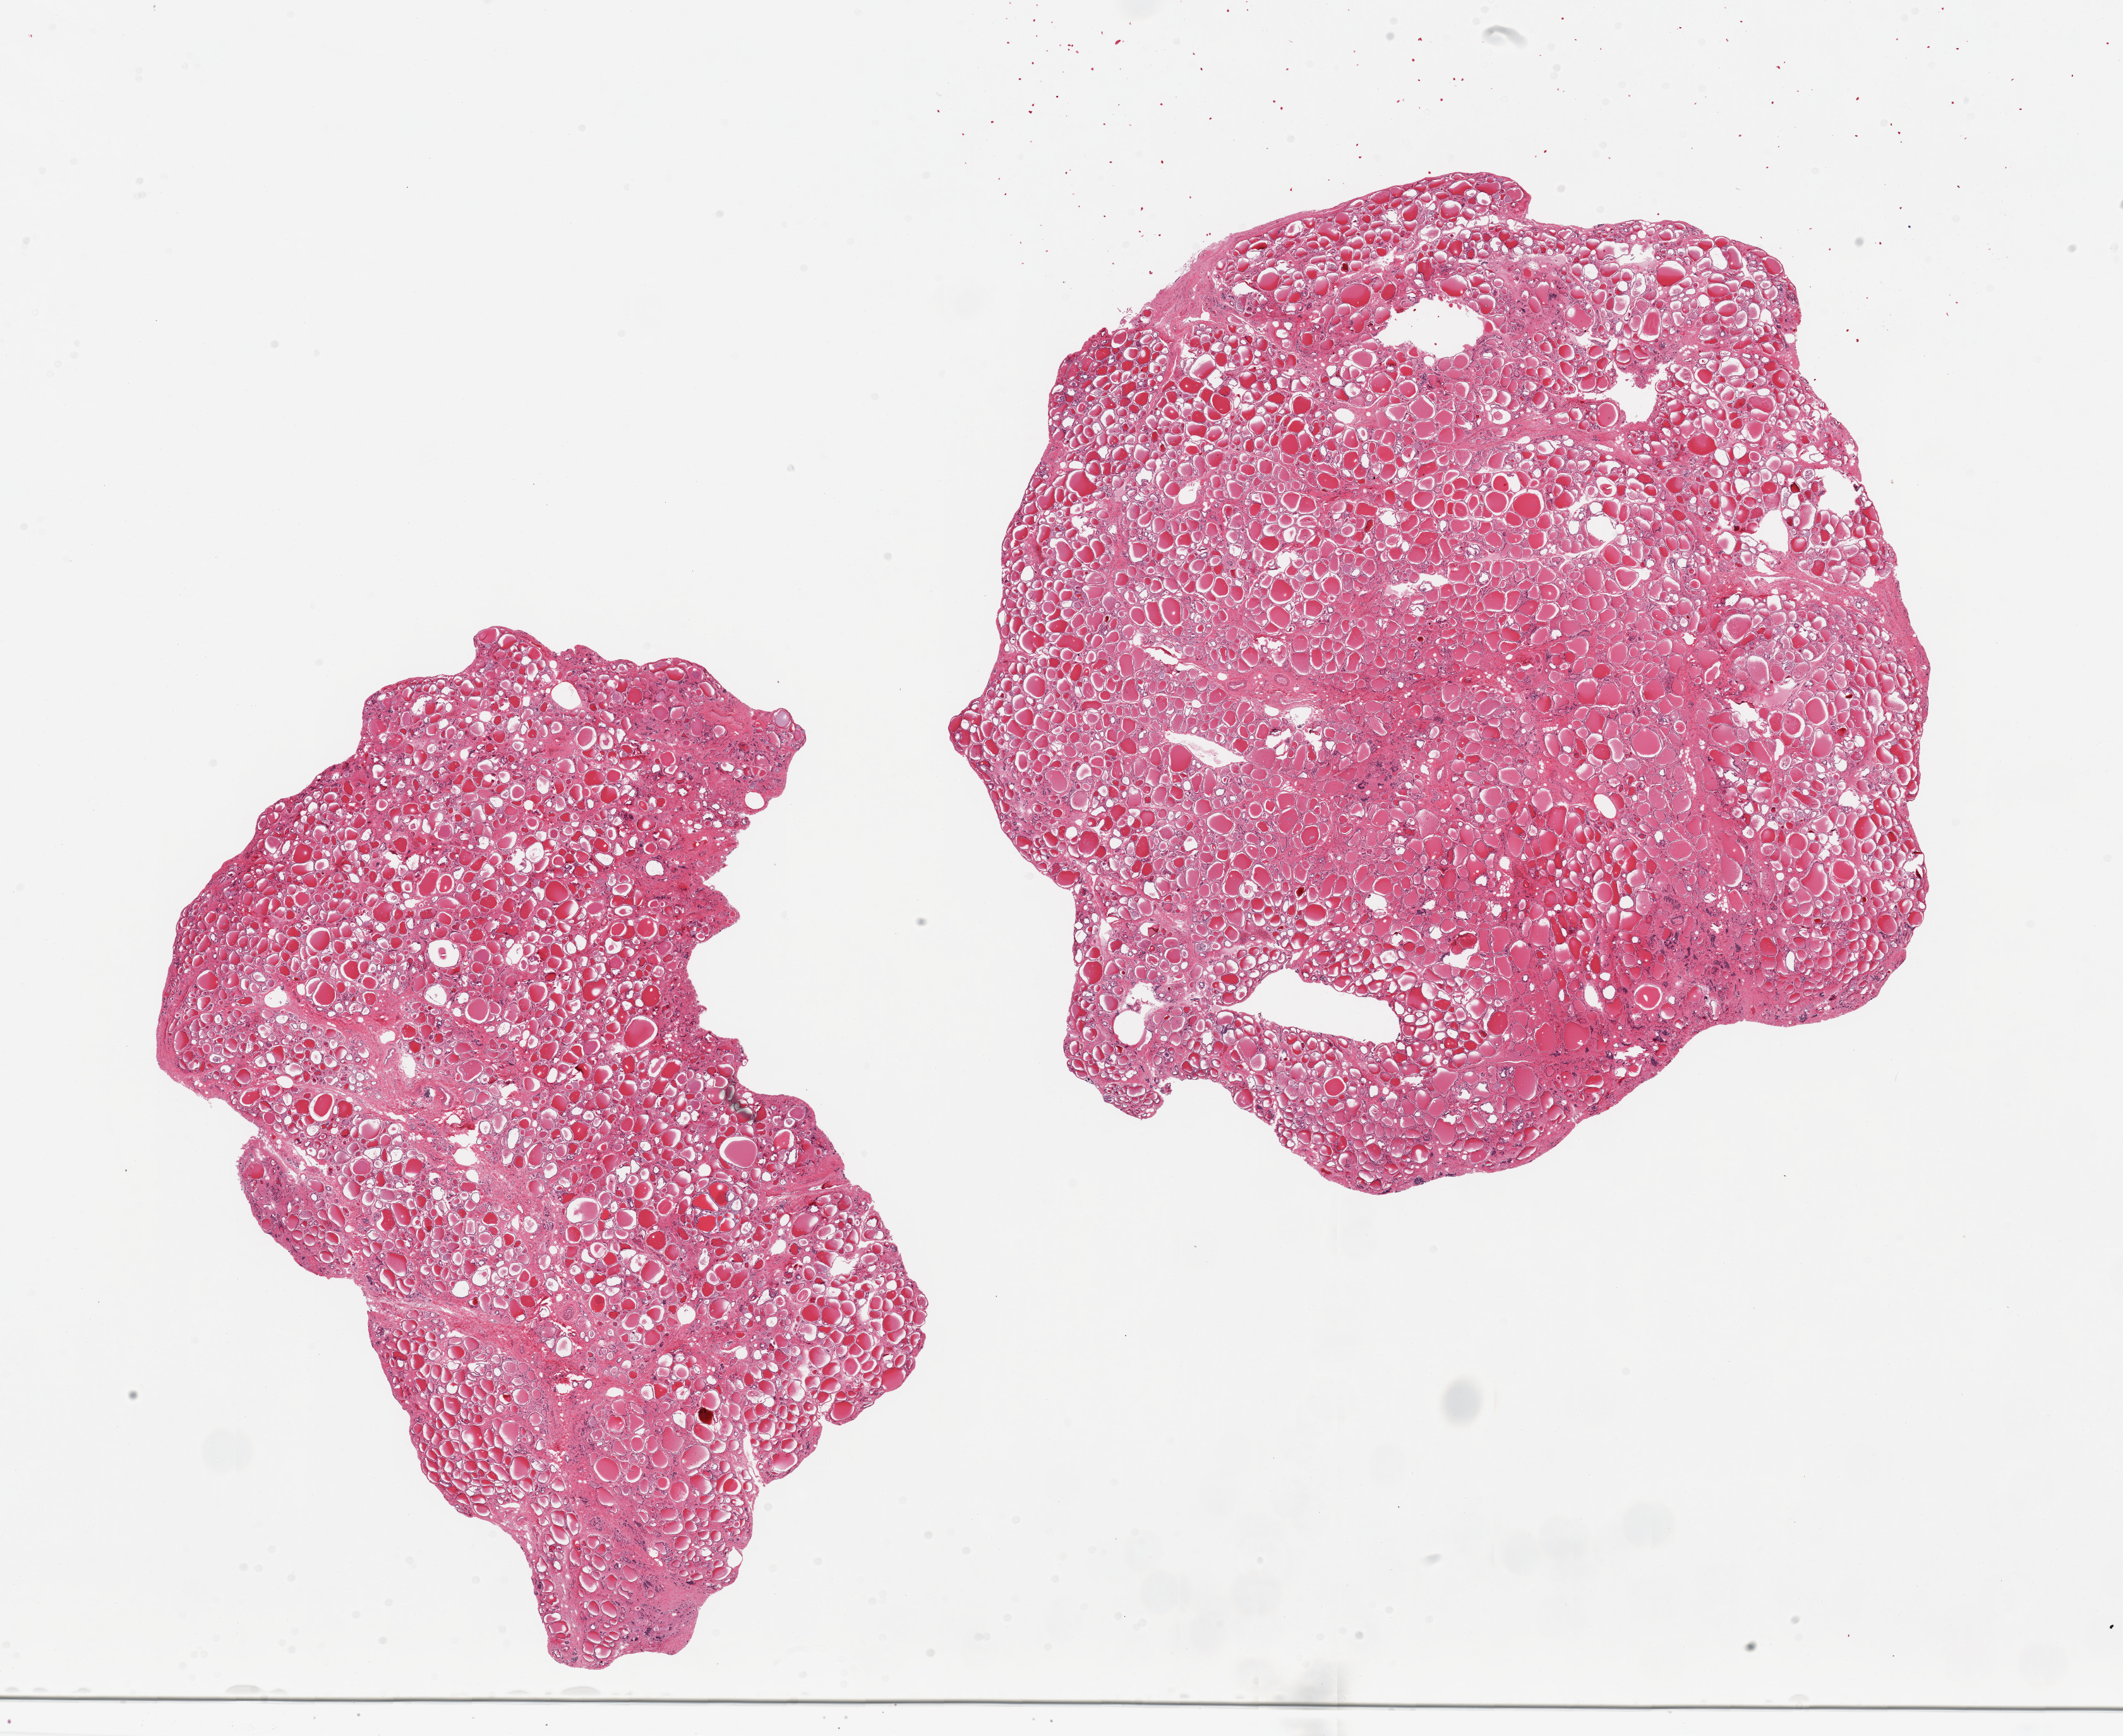
Haematoxylin and eosin whole-slide image — shown as a low-resolution overview of the whole scanned area (about 26.6 x 21.7 mm). PAXgene-fixed, paraffin-embedded tissue. Section of thyroid (target tissue). Donor tissue sample. Donor: male.
Pathologist's review note for this sample: 2 pieces, no abnormalities.